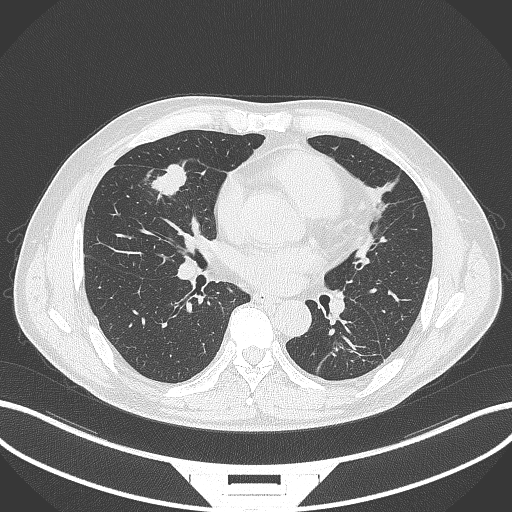
Chest CT, one axial slice; position 145 of 399 along the scan axis; lung window (W 1500 / L -600 HU); 1 mm slice thickness; 512 × 512 image matrix. Male patient, age 59 years. Case-level facts recorded for this patient, not image findings: clinical TNM (as recorded): T2a N1 M0.
Annotated regions visible in this slice (rectangle marked by the reading radiologist):
- lung tumour (recorded histology: adenocarcinoma): bounding box (x1, y1, x2, y2) in pixels: (150, 162, 190, 199)